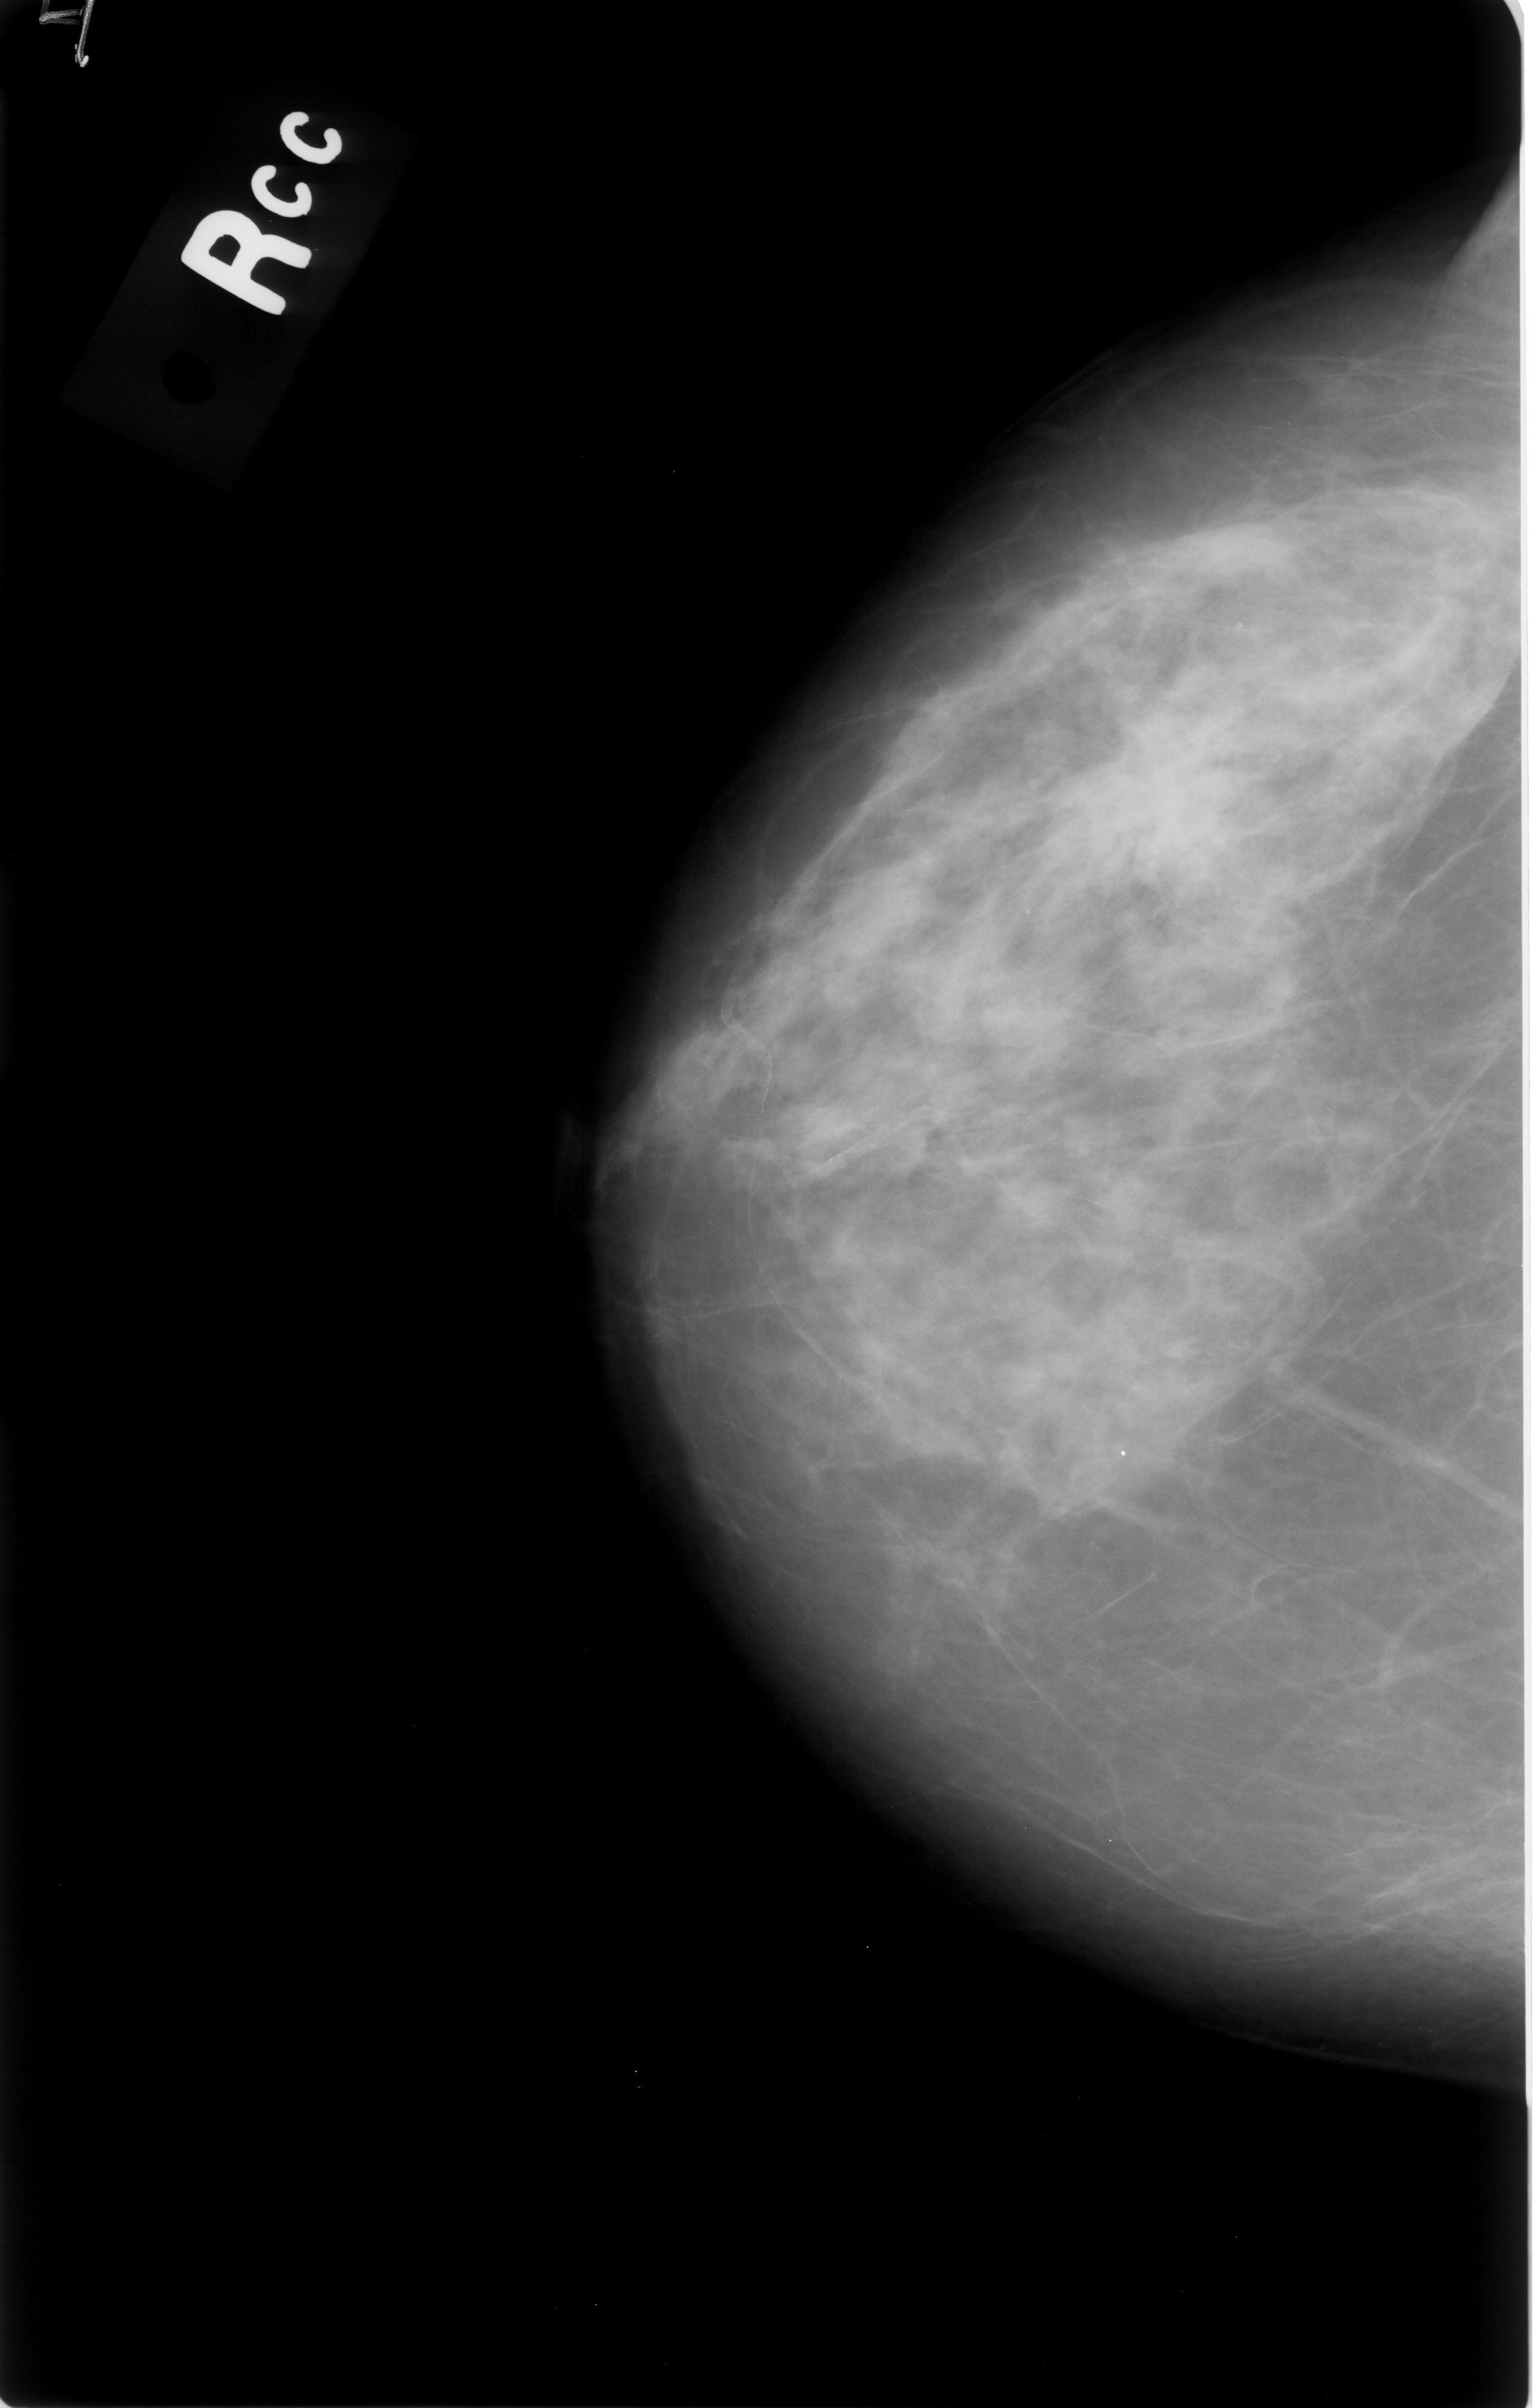
Scanned film-screen mammogram. Right breast. CC view. BI-RADS breast density category 2 (scale 1–4). 1534 × 2408 image matrix.
Marked abnormalities (boxes around the expert regions of interest):
- mass, shape irregular, margins spiculated; BI-RADS assessment category 5; pathology result (as recorded, not read from the image): malignant: box from (x=1048, y=692) to (x=1264, y=894) px